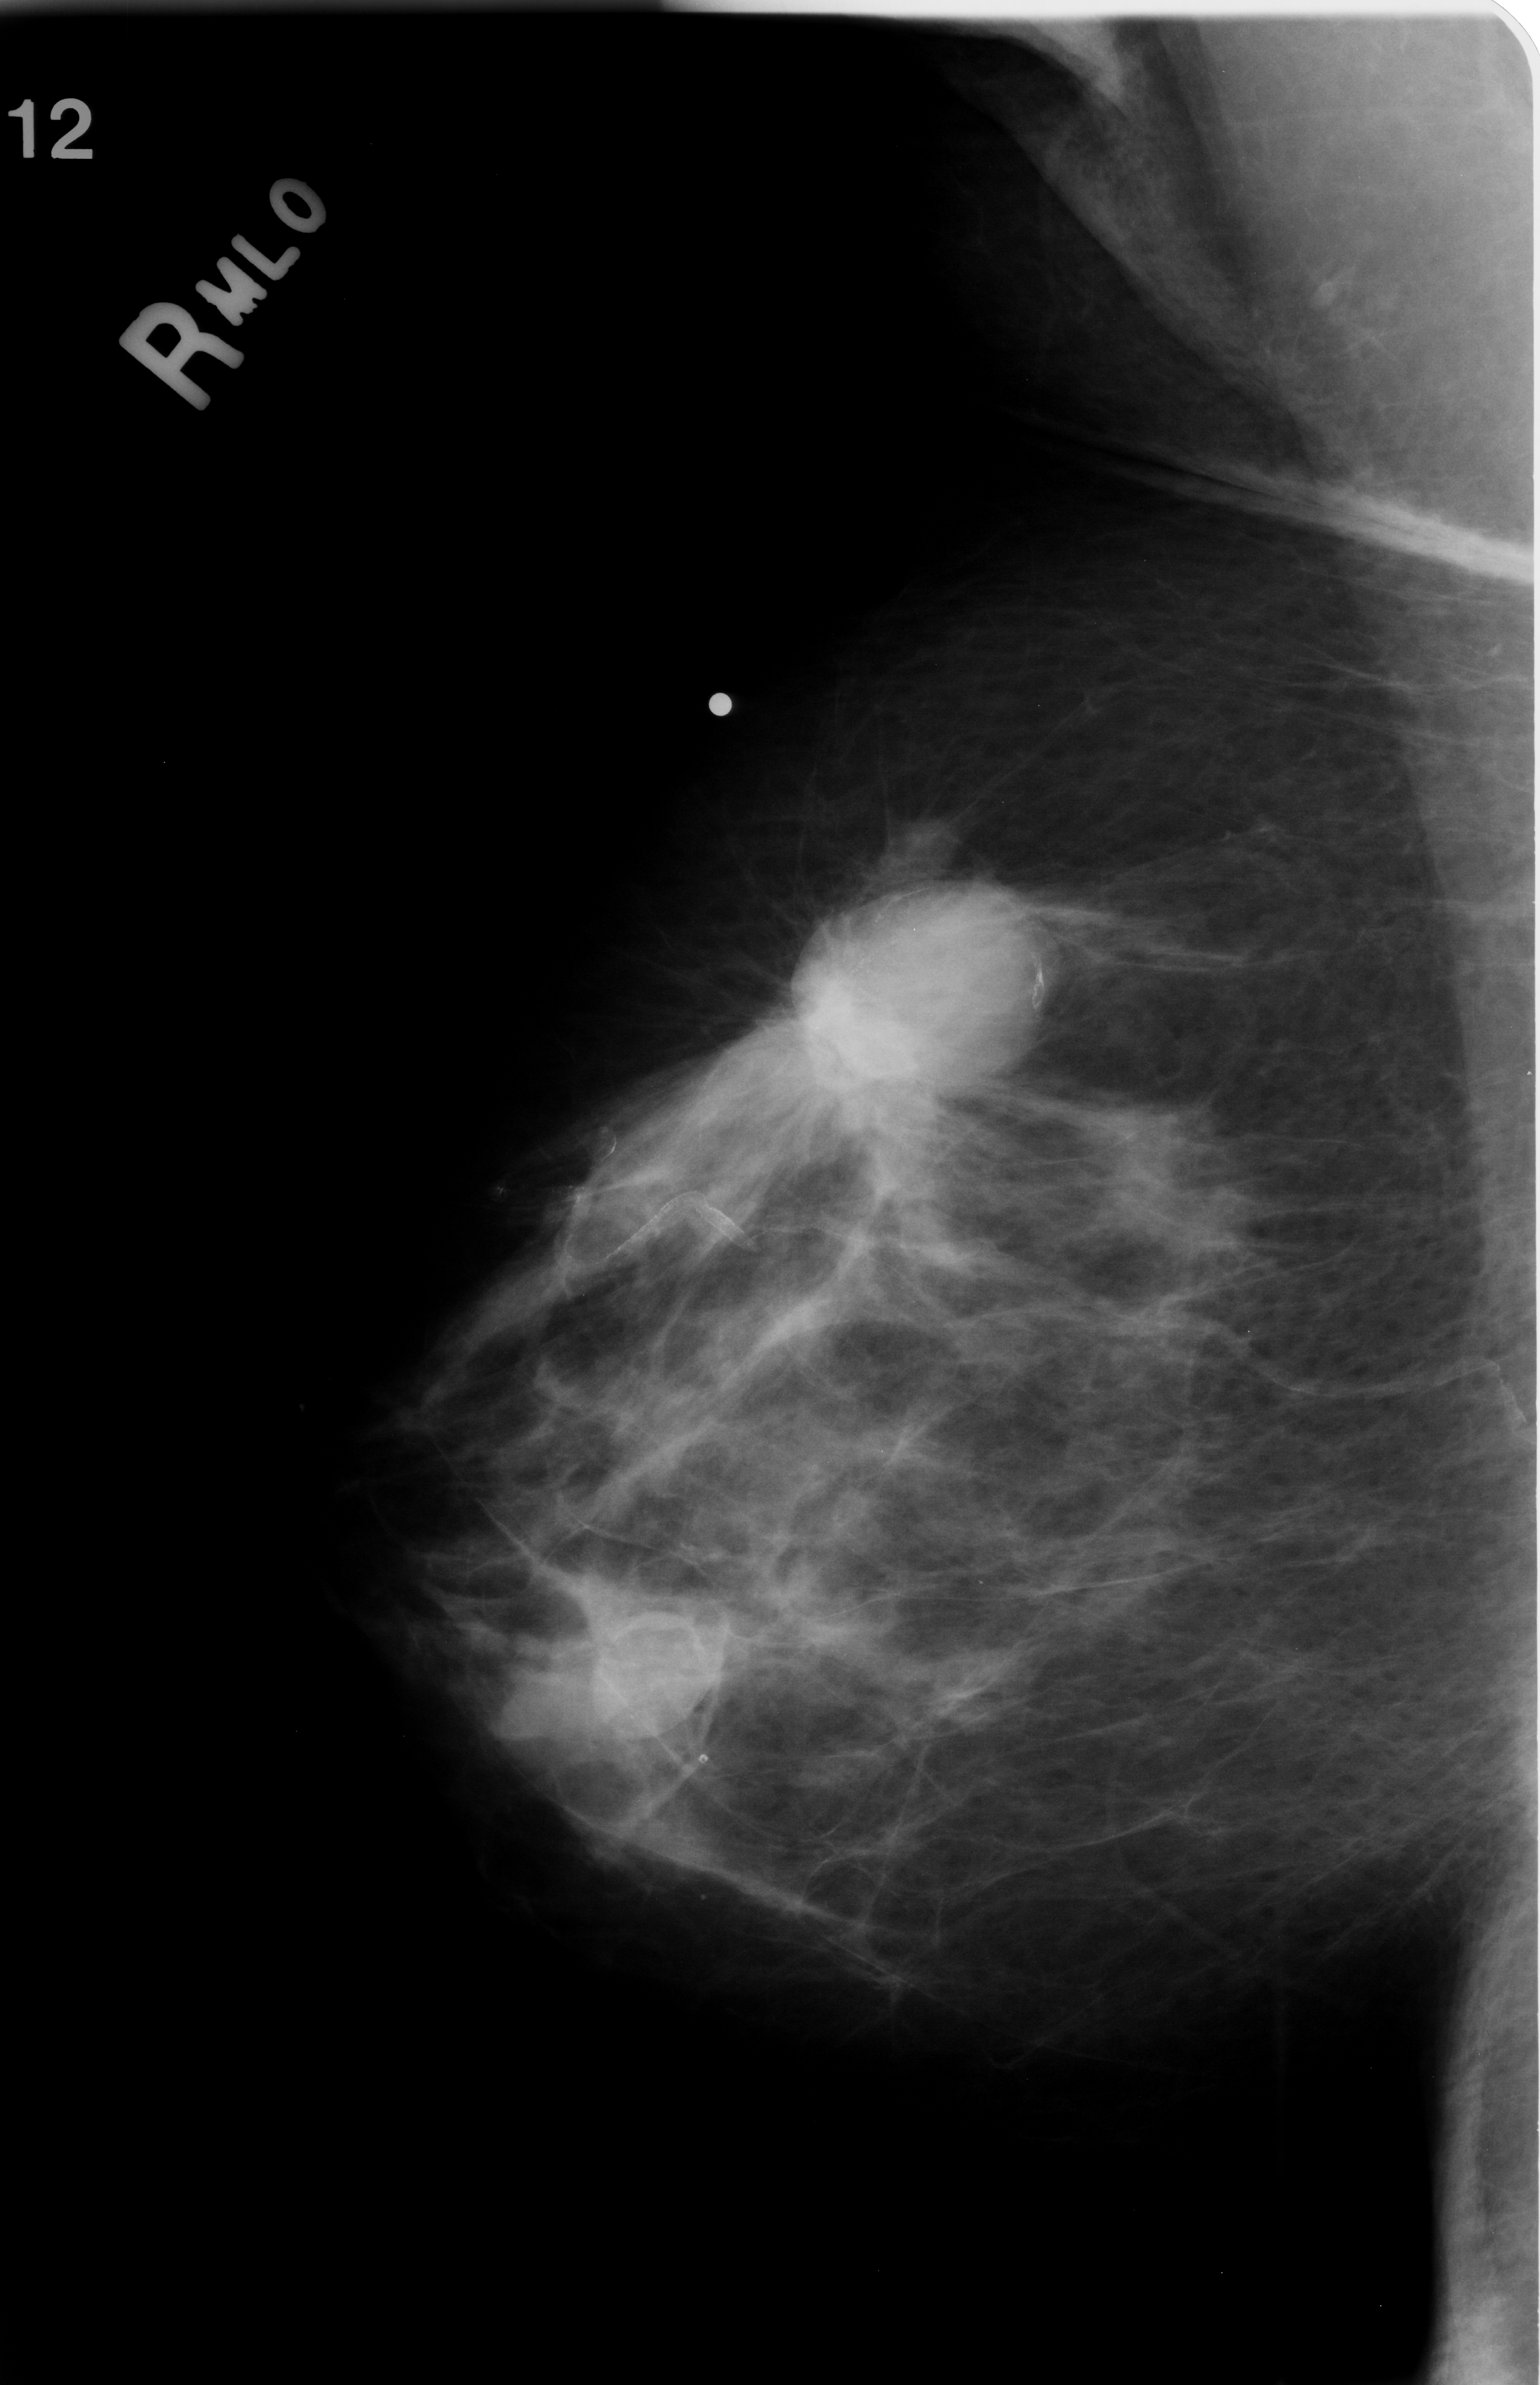
Digitized screen-film mammogram; right breast; MLO view; 1540 × 2385 image matrix.
Marked abnormalities (boxes around the expert regions of interest):
- mass, shape lobulated, margins spiculated; BI-RADS assessment category 5; pathology (as recorded): malignant: bounding box <690,807,1115,1167> (left, top, right, bottom; pixels)